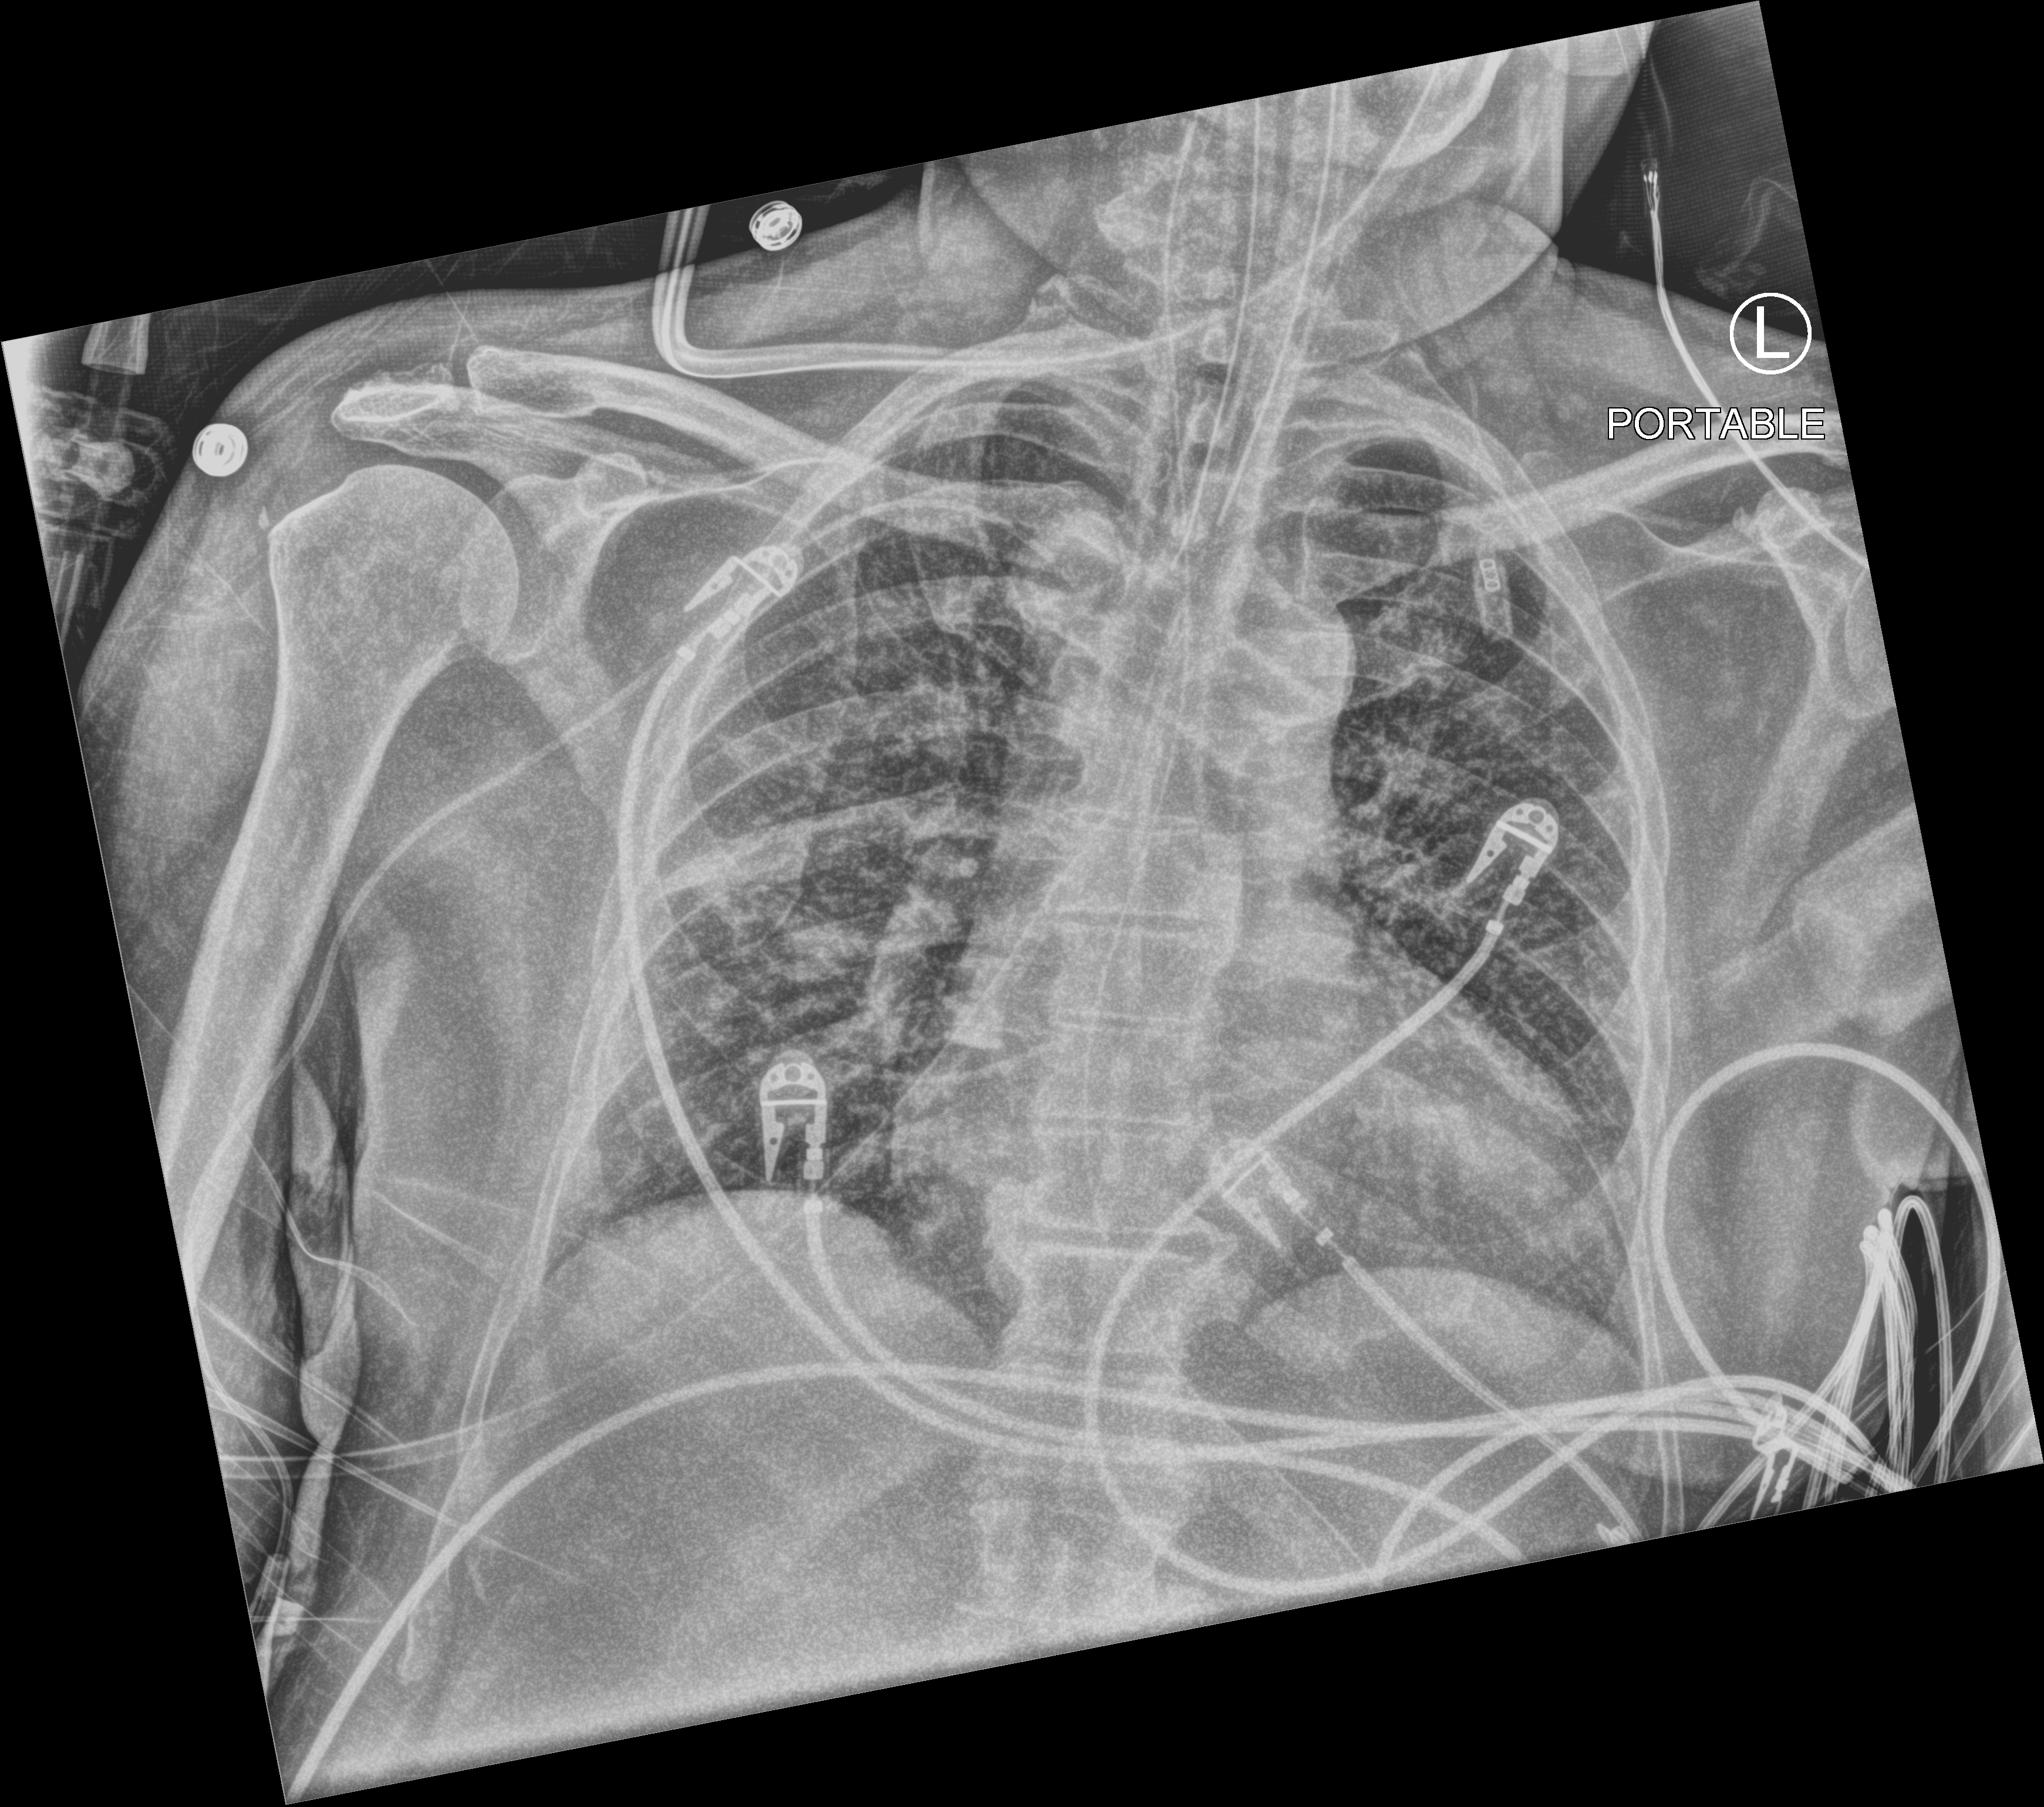
Portable chest radiograph; anteroposterior (AP) projection. Male patient hospitalised with COVID-19, age 60–74 years.
From the hospital-stay record, not from the radiograph (when in the stay this image was taken is not recorded): diabetes (admission record): no; chronic kidney disease (admission record): no.